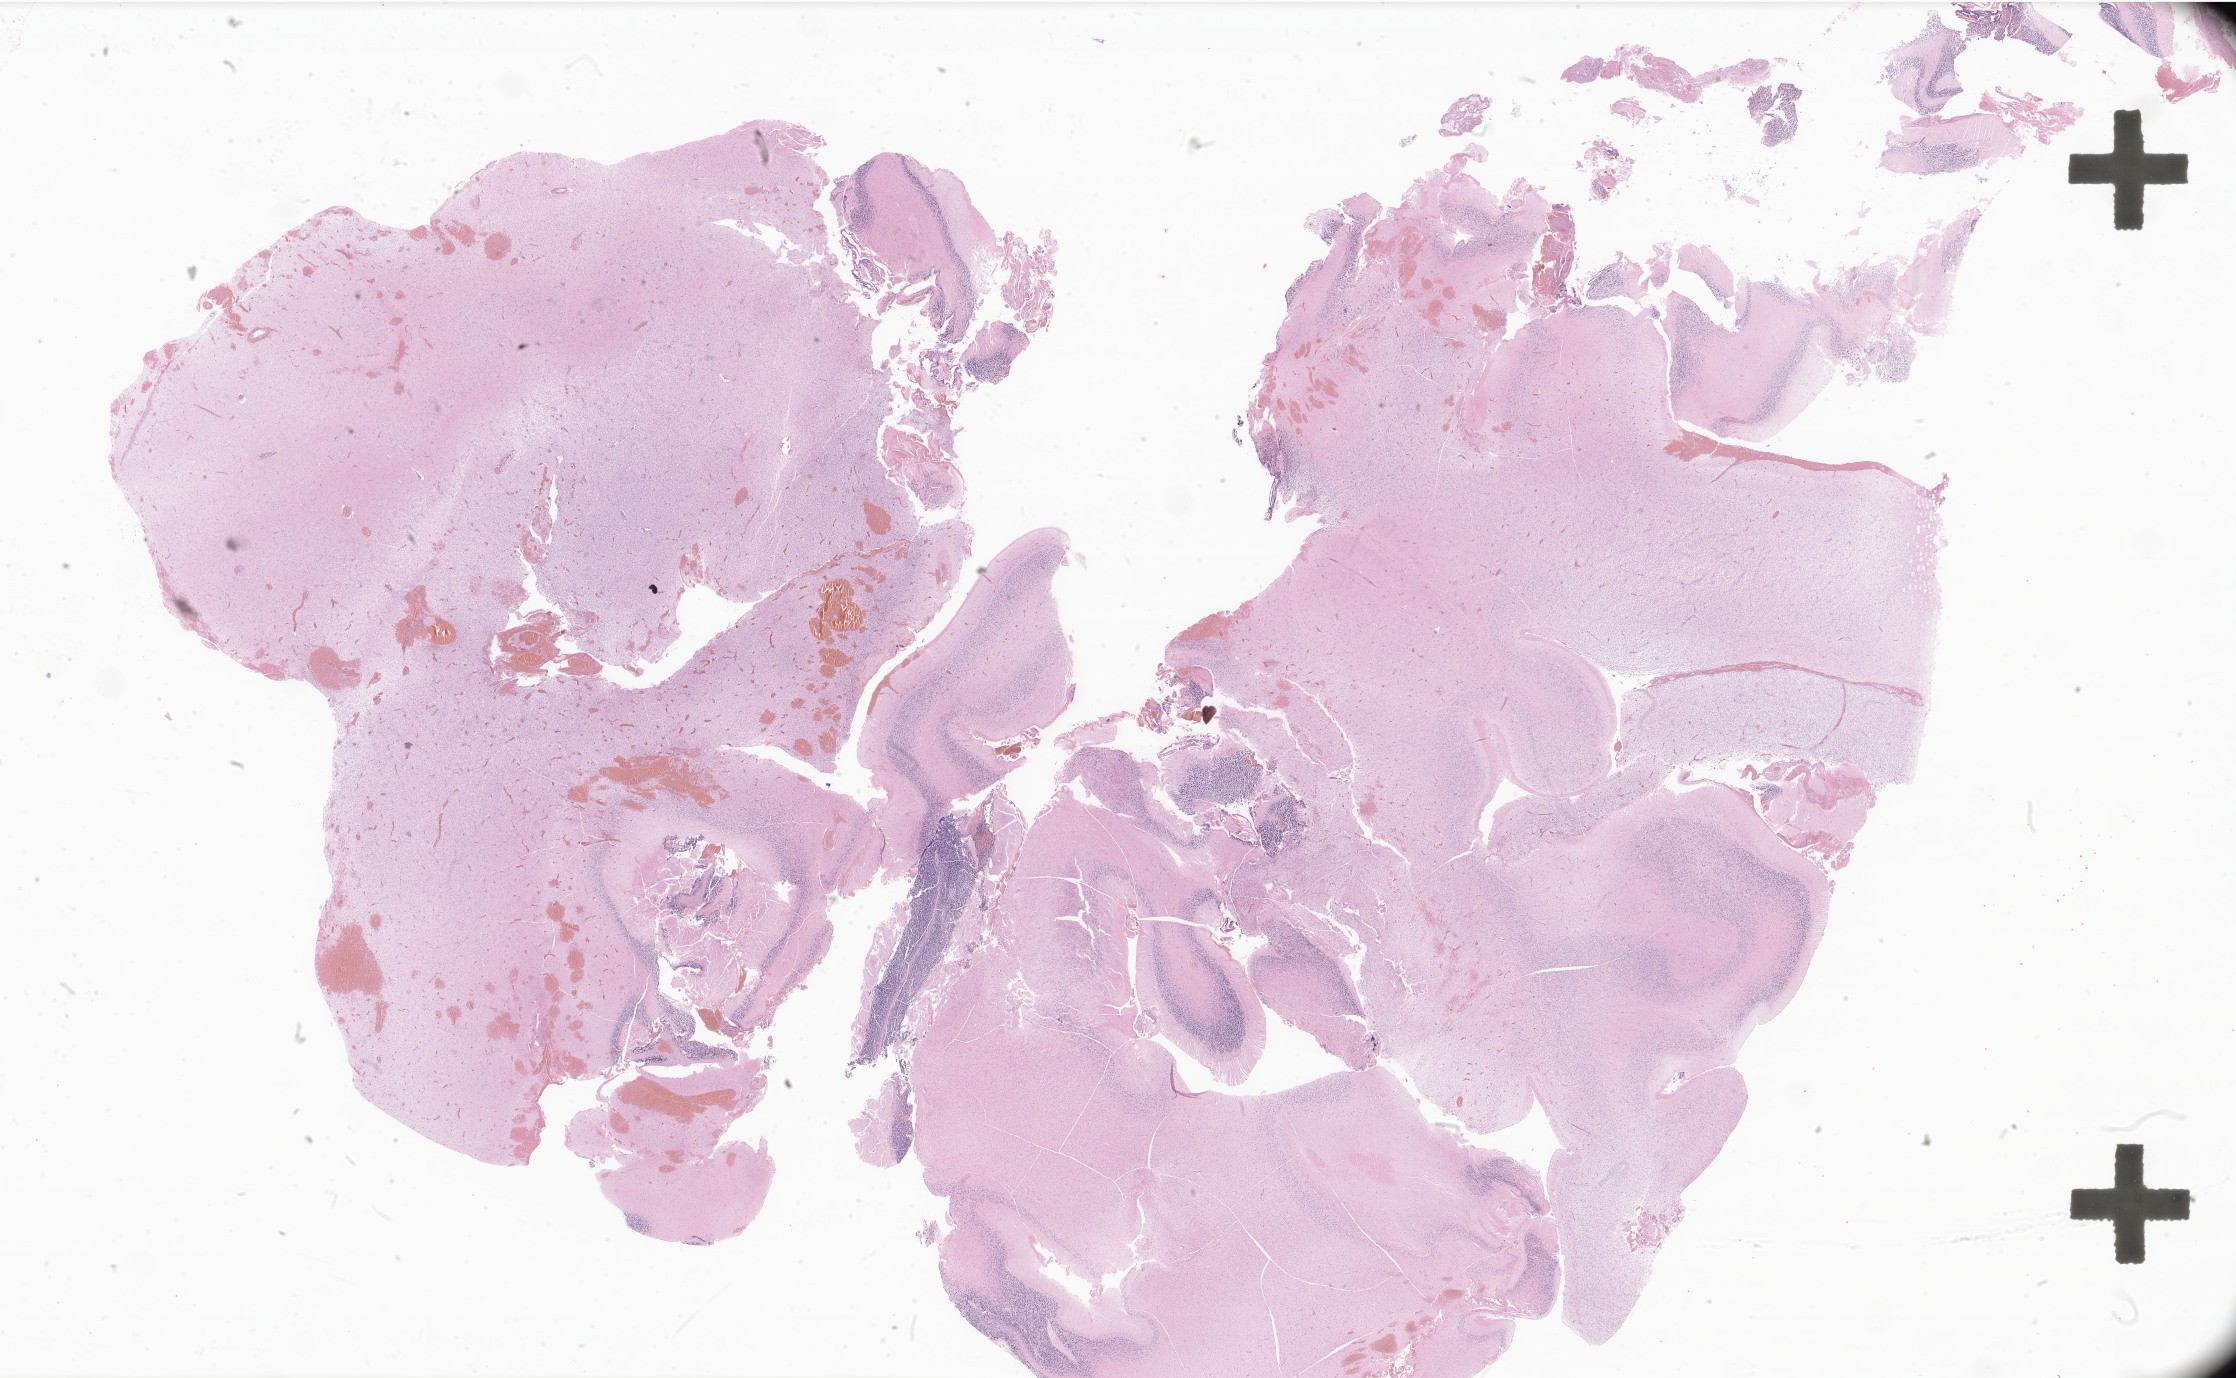
Haematoxylin and eosin whole-slide image of tumor tissue from the cerebellum, low-resolution overview of the scanned area, about 37.7 x 23.2 mm. FFPE section. Female patient, age 961 days (about 2.6 years).
* recorded diagnosis: Glioma, malignant